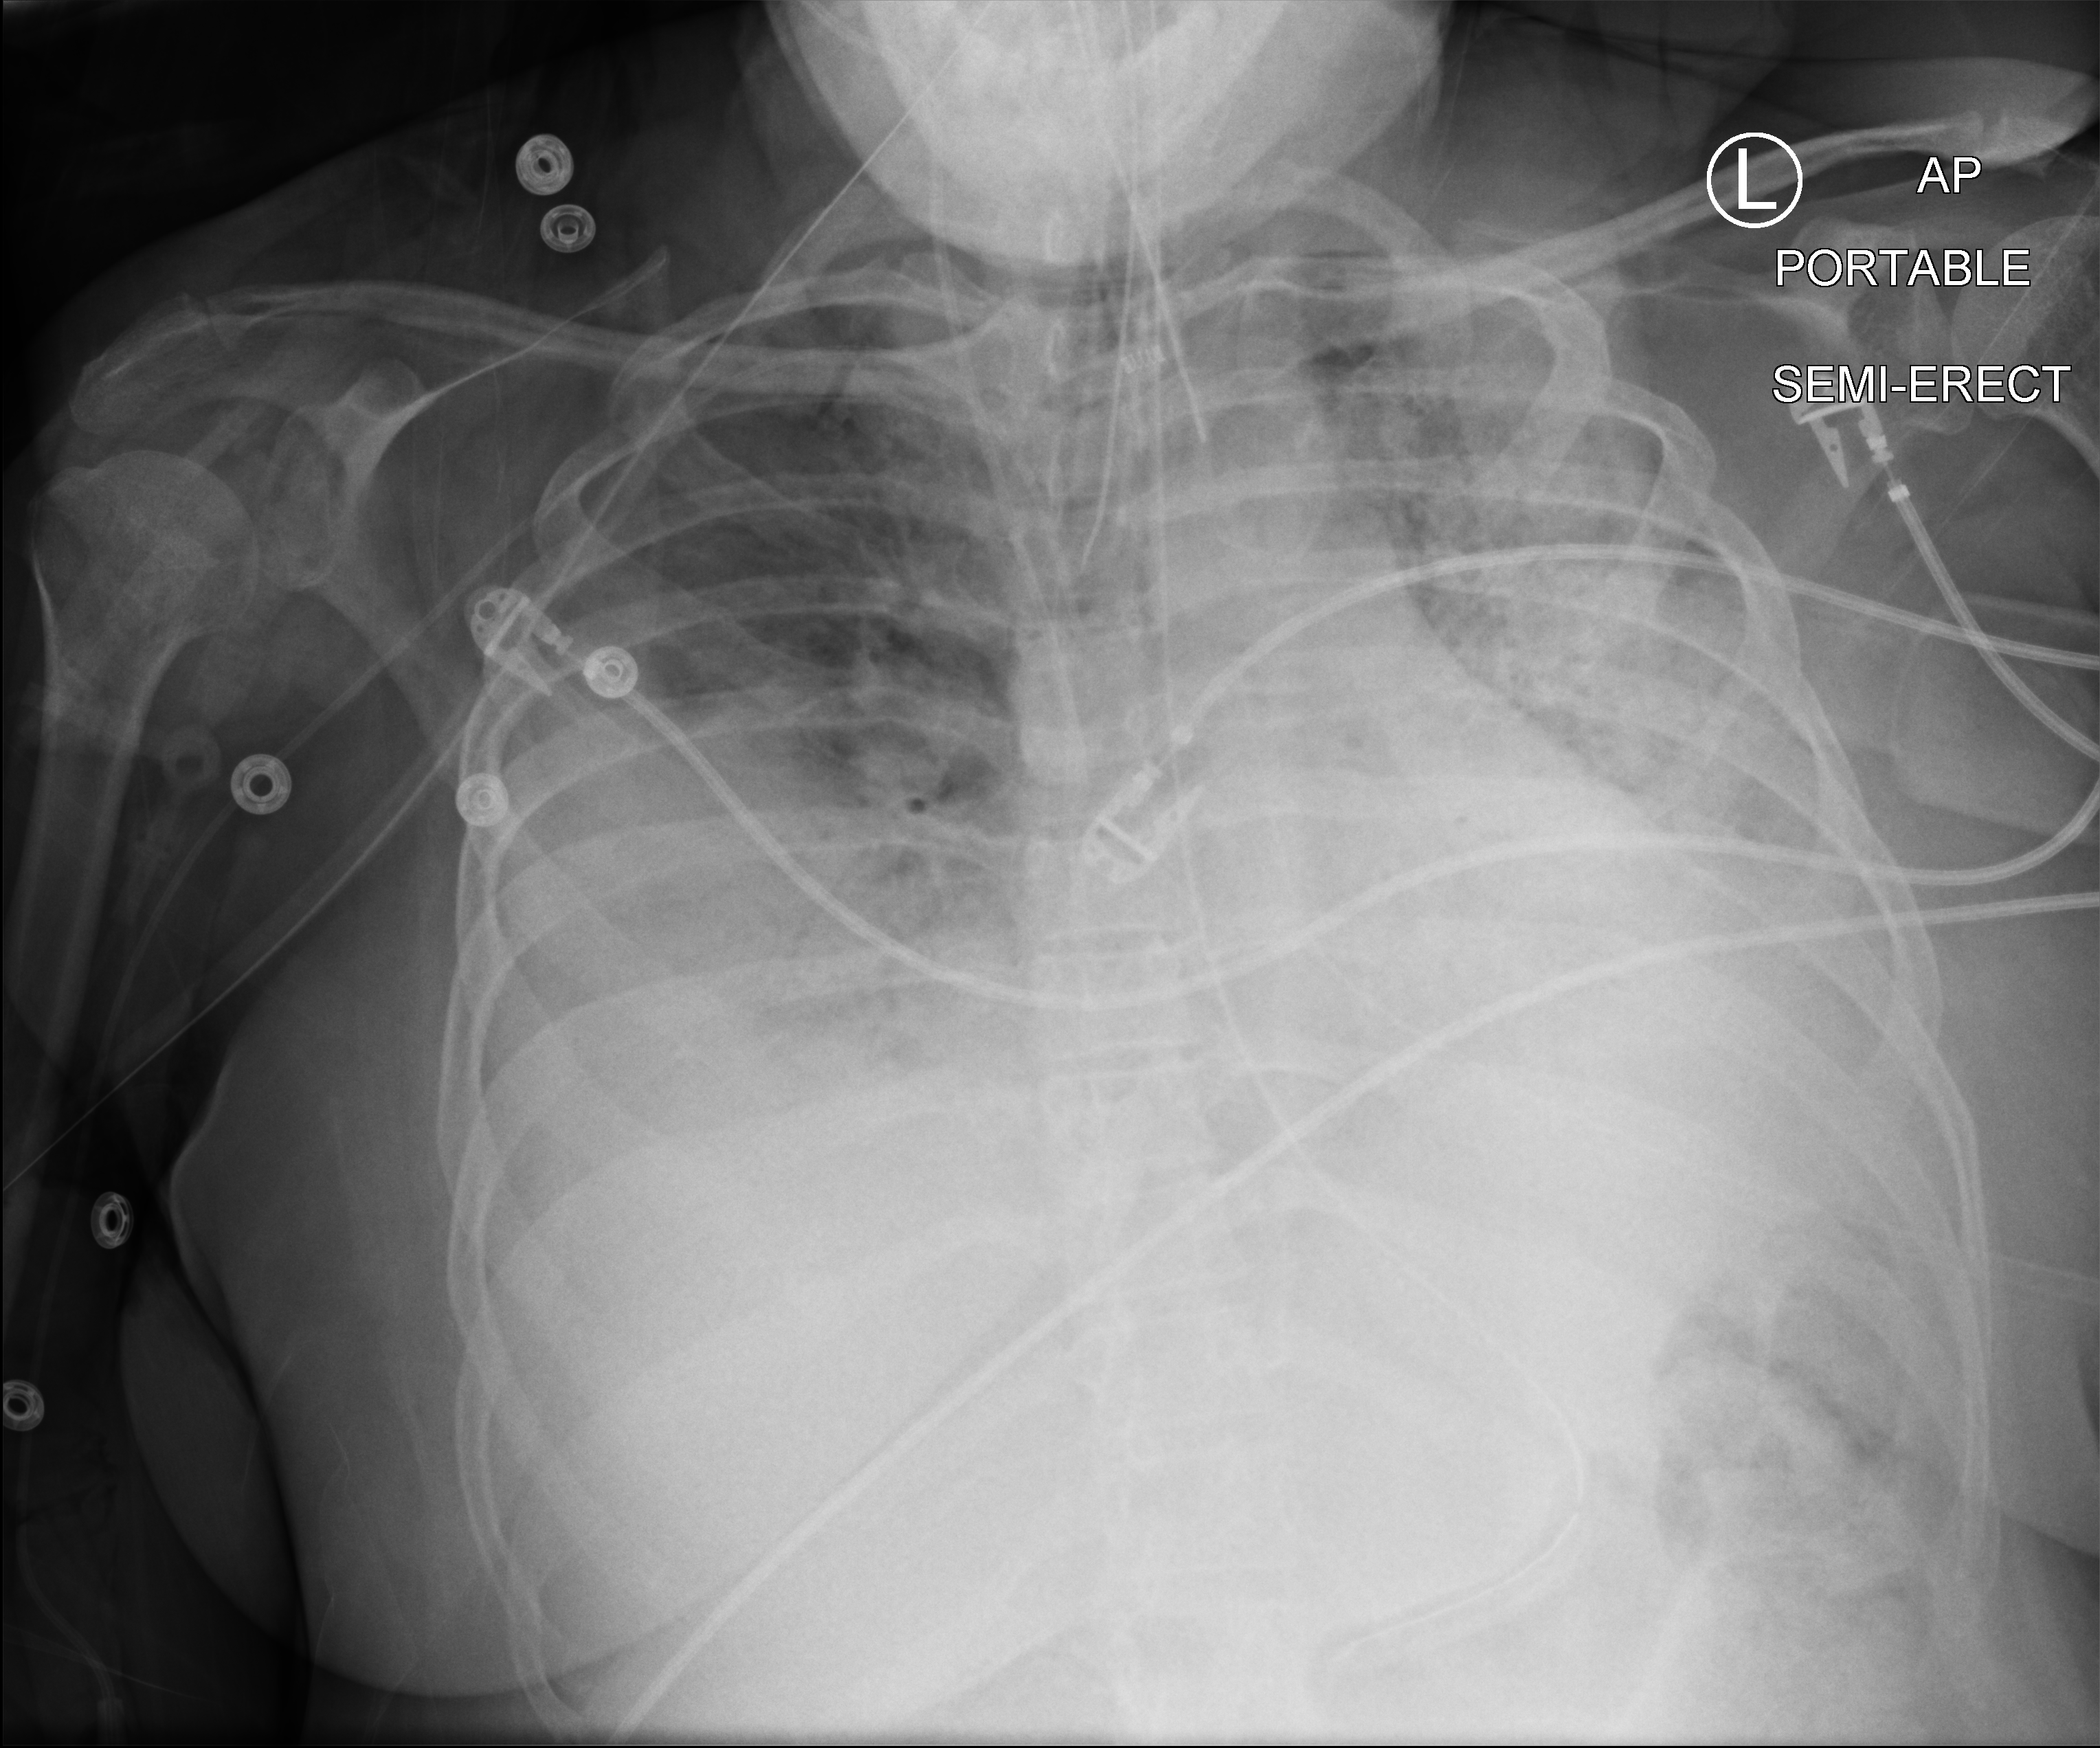
Portable chest radiograph; anteroposterior (AP) projection. Adult patient hospitalised with COVID-19, age 18–59 years.
Hospital-stay facts (about this admission, not read from this image; timing relative to this image not recorded):
- mechanically ventilated during this hospital stay: yes
- COPD (admission record): no
- admitted to intensive care during this hospital stay: yes